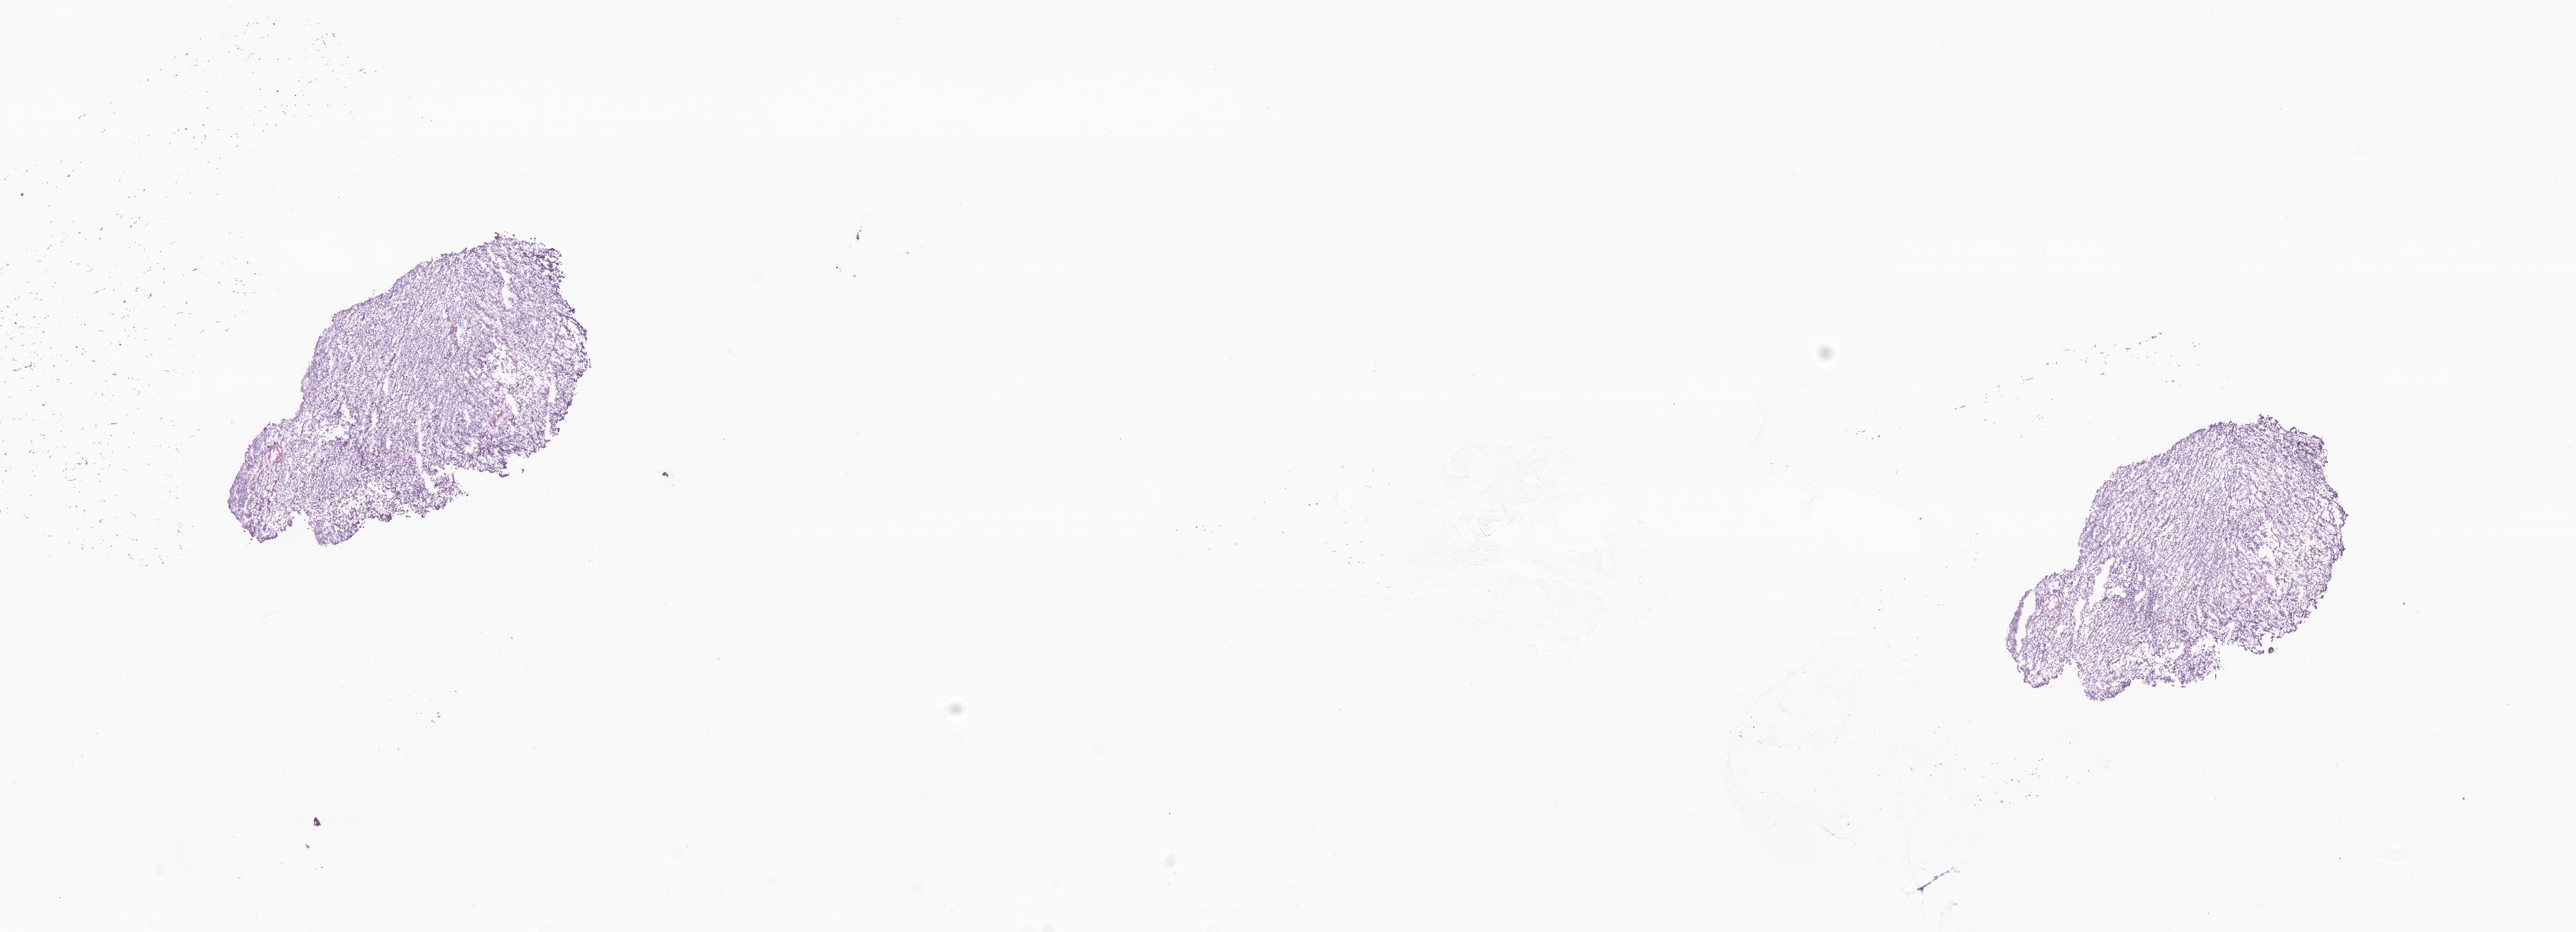
Whole-slide image, hematoxylin and eosin (H&E) stain of tumor tissue from the cerebellum, a low-resolution overview of the entire scanned area, about 20.7 x 7.5 mm; frozen section. Male patient, age 174 months (14 years 6 months).
* recorded diagnosis: Medulloblastoma, NOS